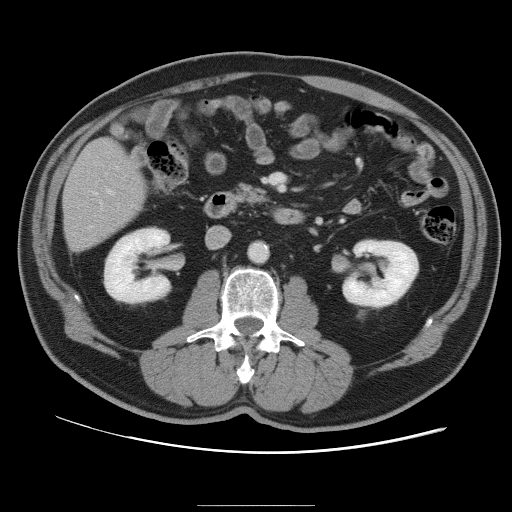
Contrast-enhanced abdominal CT, one axial slice; slice 32 of 105 in the series (ordered by position); 120 kVp; soft-tissue window (W 400 / L 40 HU); 512 × 512 image matrix, field of view 399 × 399 mm. Male patient, age 64 years. From the clinical record (not read from this slice): diagnosis: colorectal cancer liver metastases, imaged before liver resection; multiple liver metastases: yes; largest metastasis: 3 cm; disease in both lobes: yes.
Outlined on this slice (manually delineated by an expert):
- hepatic veins: box from (x=108, y=190) to (x=112, y=194) px
- liver: (x=64, y=140)–(x=145, y=251)
- planned liver remnant (the part of the liver to remain after resection): (x=64, y=140)–(x=146, y=233)
- portal vein (with intrahepatic branches): (x=94, y=192)–(x=98, y=195)